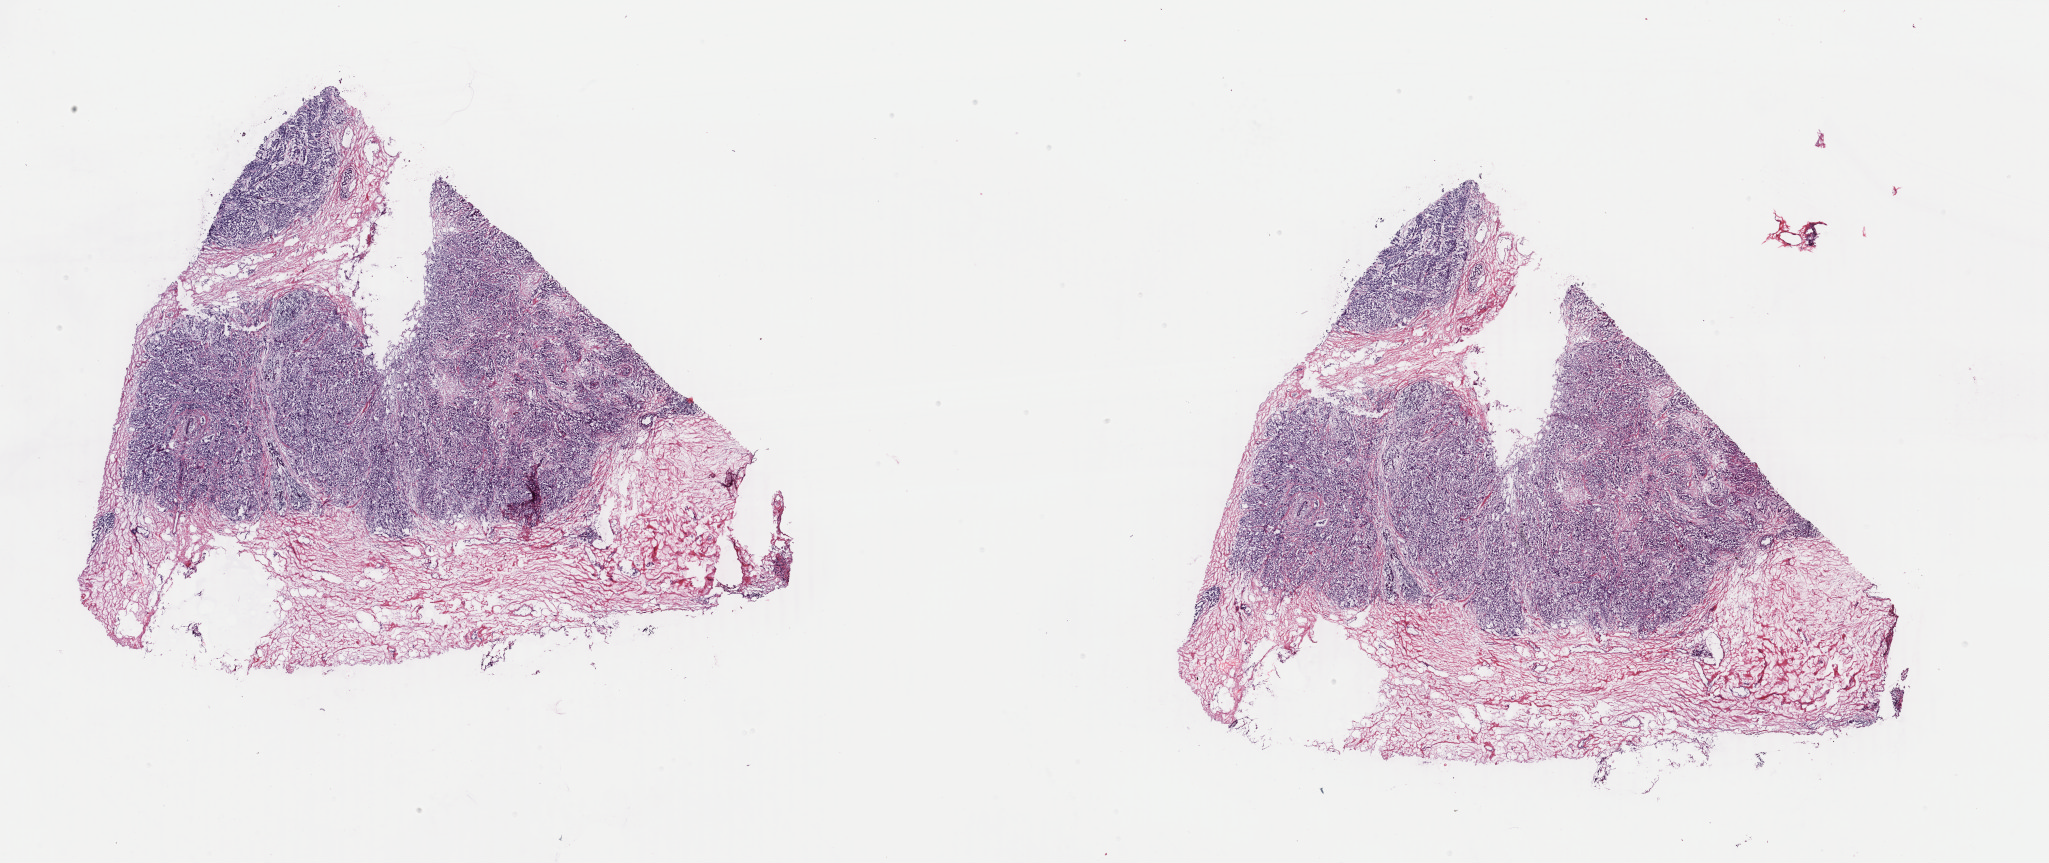
H&E whole-slide image, shown as a low-resolution overview of the whole scanned area (about 32.6 x 13.7 mm), frozen section from the top of the tissue portion, primary tumour sample from the breast. Female patient; age at initial diagnosis 59 years. Pathologist review of this section (percent, as recorded): tumour cells 85%, tumour nuclei 85%, normal cells 2%, stromal cells 13%, necrosis 0%. Inflammatory infiltration, as recorded: lymphocyte infiltration 1%, monocyte infiltration 0%, neutrophil infiltration 0%.
Pathologic diagnosis: Infiltrating duct carcinoma, NOS. Laterality: left. Lymph nodes positive (case pathology): 3 of 27 examined. TNM: T3 N1a M0. AJCC pathologic stage: IIIA.